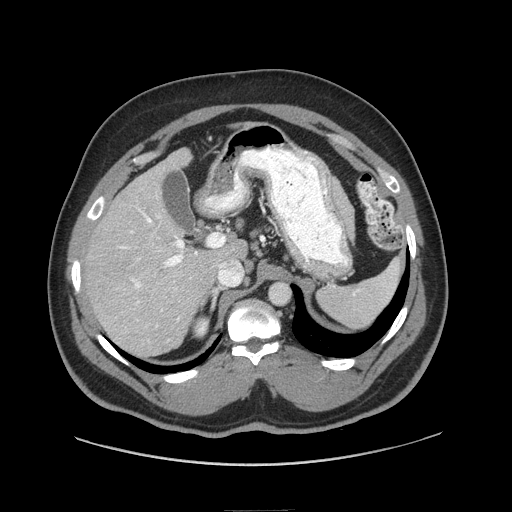
Contrast-enhanced abdominal CT (liver protocol), one axial slice; position 49 of 87 along the scan axis; reconstruction kernel STANDARD; 140 kVp; soft-tissue window (W 400 / L 40 HU); 512 × 512 image matrix, field of view 440 × 440 mm. Case-level facts recorded for this patient, not image findings: diagnosis: hepatocellular carcinoma (patient treated with transarterial chemoembolisation; whether this scan precedes or follows treatment is not stated here); TNM stage (as recorded): Stage-II; Child-Pugh class: A; tumour nodularity: uninodular.
Outlined on this slice (semi-automatically segmented with operator editing):
- liver parenchyma outside the tumour (the mass and vessels are separate outlines, so this box may not span the whole liver): bounding box (x1, y1, x2, y2) in pixels: (84, 148, 246, 356)
- liver vessels: (119, 208, 234, 327)